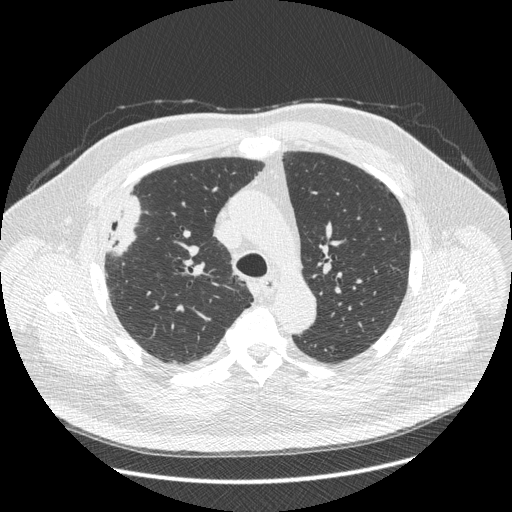
Axial slice from a low-dose chest CT screening exam; third screening round (two years after baseline); lung window (W 1500 / L -600 HU); 512 × 512 image matrix. Male participant, aged 66 years at enrolment. Current smoker at enrolment.
Lesion marked by an expert reader, bounding box (x1, y1, x2, y2) in pixels: (87, 200, 147, 269). The exam's reader record, not a measurement of the box and not confirmed to be the same lesion: non-calcified nodule or mass ≥4 mm, right upper lobe, 48 × 25 mm, spiculated (stellate) margins, soft tissue attenuation, pre-existing on the prior screen: no. Participant outcome: lung cancer diagnosed 35 days after this screen — non-small cell carcinoma, right upper lobe, stage IV (AJCC 6th edition), 50 mm at pathology.